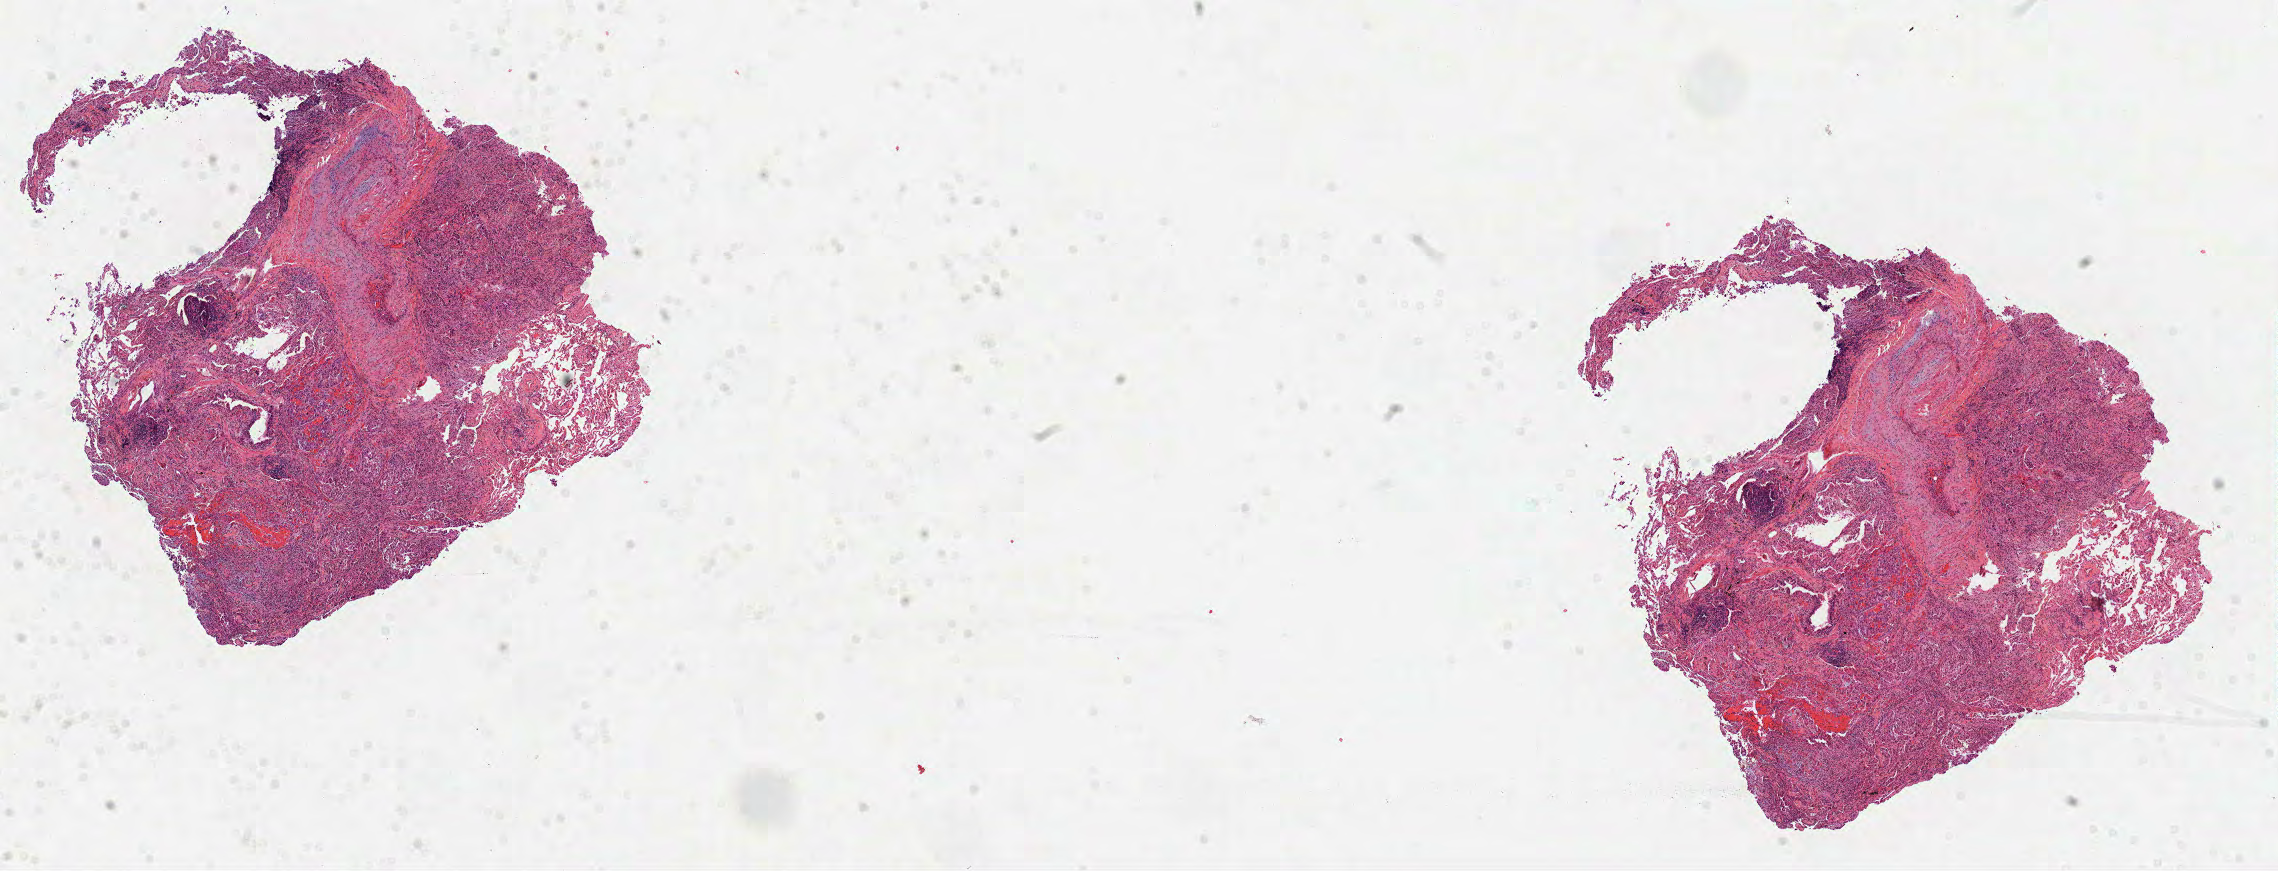
Whole-slide histology image, H&E-stained, shown as a low-resolution overview of the whole scanned area (about 18.4 x 7.0 mm, acquisition: 40x scan), formalin-fixed paraffin-embedded (FFPE) diagnostic section, primary tumour sample from the lung. Patient: female, age at initial diagnosis 74 years.
AJCC pathologic stage: IV (7th edition). TNM: TX NX M1. Histologic diagnosis: Adenocarcinoma, NOS (upper lobe, lung).